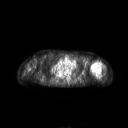
FDG PET of an extremity soft-tissue mass (from a PET/CT study), one axial slice. Slice 175 of 267 in the series (ordered by position). 3.27 mm slice thickness. 128 × 128 image matrix, field of view 700 × 700 mm. Patient: female, 83 years. From the clinical record (not read from this slice): histological type: pleiomorphic leiomyosarcoma; grade: high; site of the primary tumour: left biceps.
Annotated regions visible in this slice (expert contour drawn on MRI and transferred to this co-registered scan by the dataset authors):
- gross tumour volume including surrounding oedema: bounding box [x1, y1, x2, y2] px = [90, 59, 103, 77]
- gross tumour volume (mass): [90, 60, 102, 75]